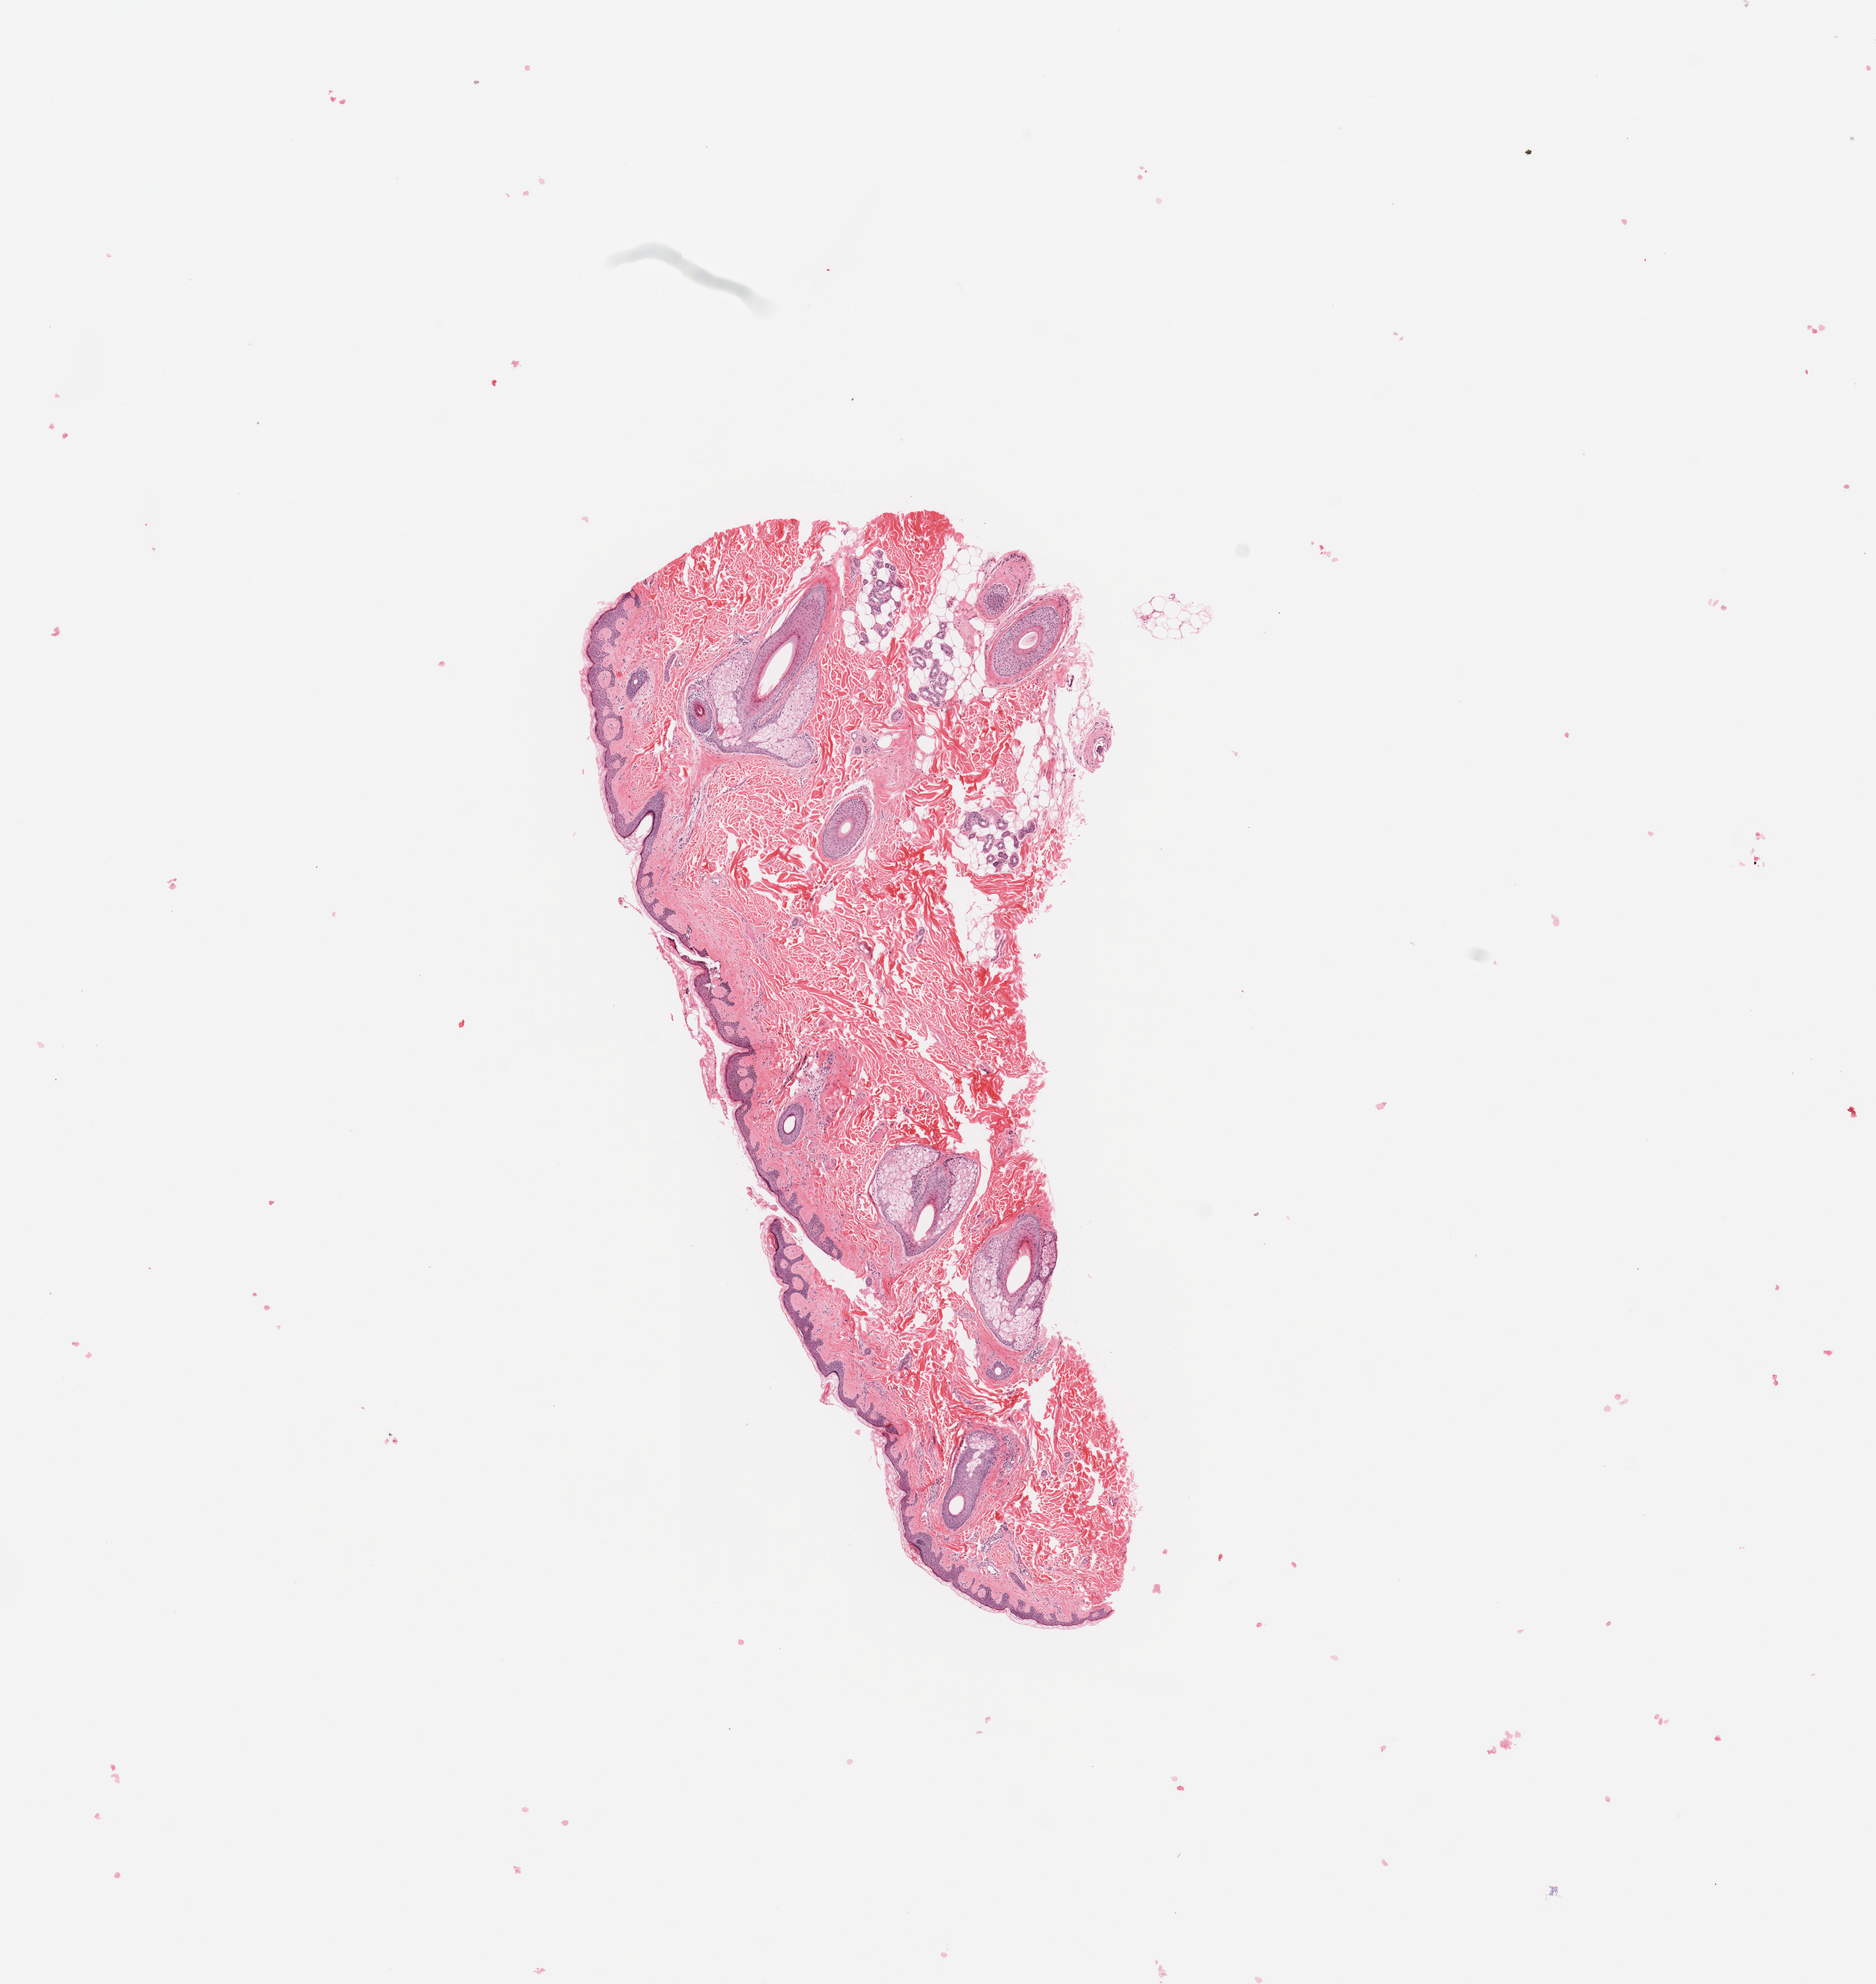
H&E whole-slide image — low-resolution overview of the scanned area, about 10.8 x 11.5 mm; normal (non-tumour) tissue (melanoma cohort); sampled site not recorded. 73-year-old female patient.
• this section: normal (non-tumour) tissue from the same patient
• patient diagnosis: Malignant melanoma, NOS